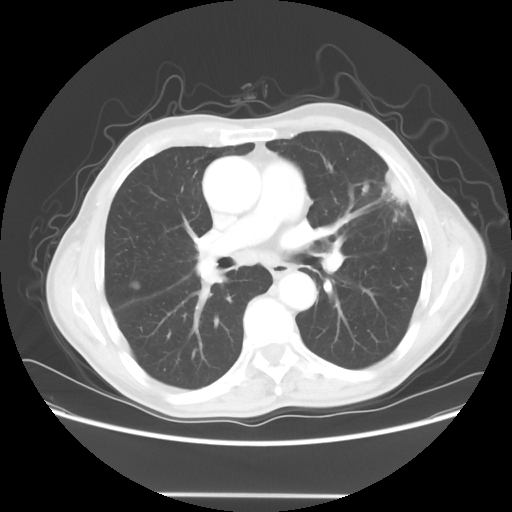
Chest CT, one axial slice; position 35 of 64 along the scan axis; 120 kVp; lung window (W 1500 / L -600 HU); 5 mm slice thickness; 512 × 512 image matrix, field of view 392 × 392 mm. Male patient, age 71 years. From the clinical record (not read from this slice): clinical TNM (as recorded): T1c N0 M0.
Structures marked on this image (bounding box drawn by a radiologist):
- lung tumour (recorded histology: adenocarcinoma): bounding box <378,164,417,215> (left, top, right, bottom; pixels)